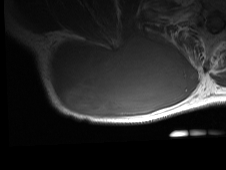
MRI of an extremity soft-tissue mass, one axial slice; position 45 of 81 along the scan axis; MR volume resampled by the dataset authors to the PET/CT grid (not the native acquisition matrix); 3.27 mm slice thickness; 226 × 170 image matrix, field of view 221 × 166 mm. Male patient. From the clinical record (not read from this slice): histological type: pleiomorphic spindle cell undifferentiated; grade: high; site of the primary tumour: right parascapusular.
Outlined on this slice (expert contour drawn on MRI and transferred to this co-registered scan by the dataset authors):
- gross tumour volume including surrounding oedema: bounding box <46,33,200,119> (left, top, right, bottom; pixels)
- gross tumour volume (mass): <48,33,187,116>